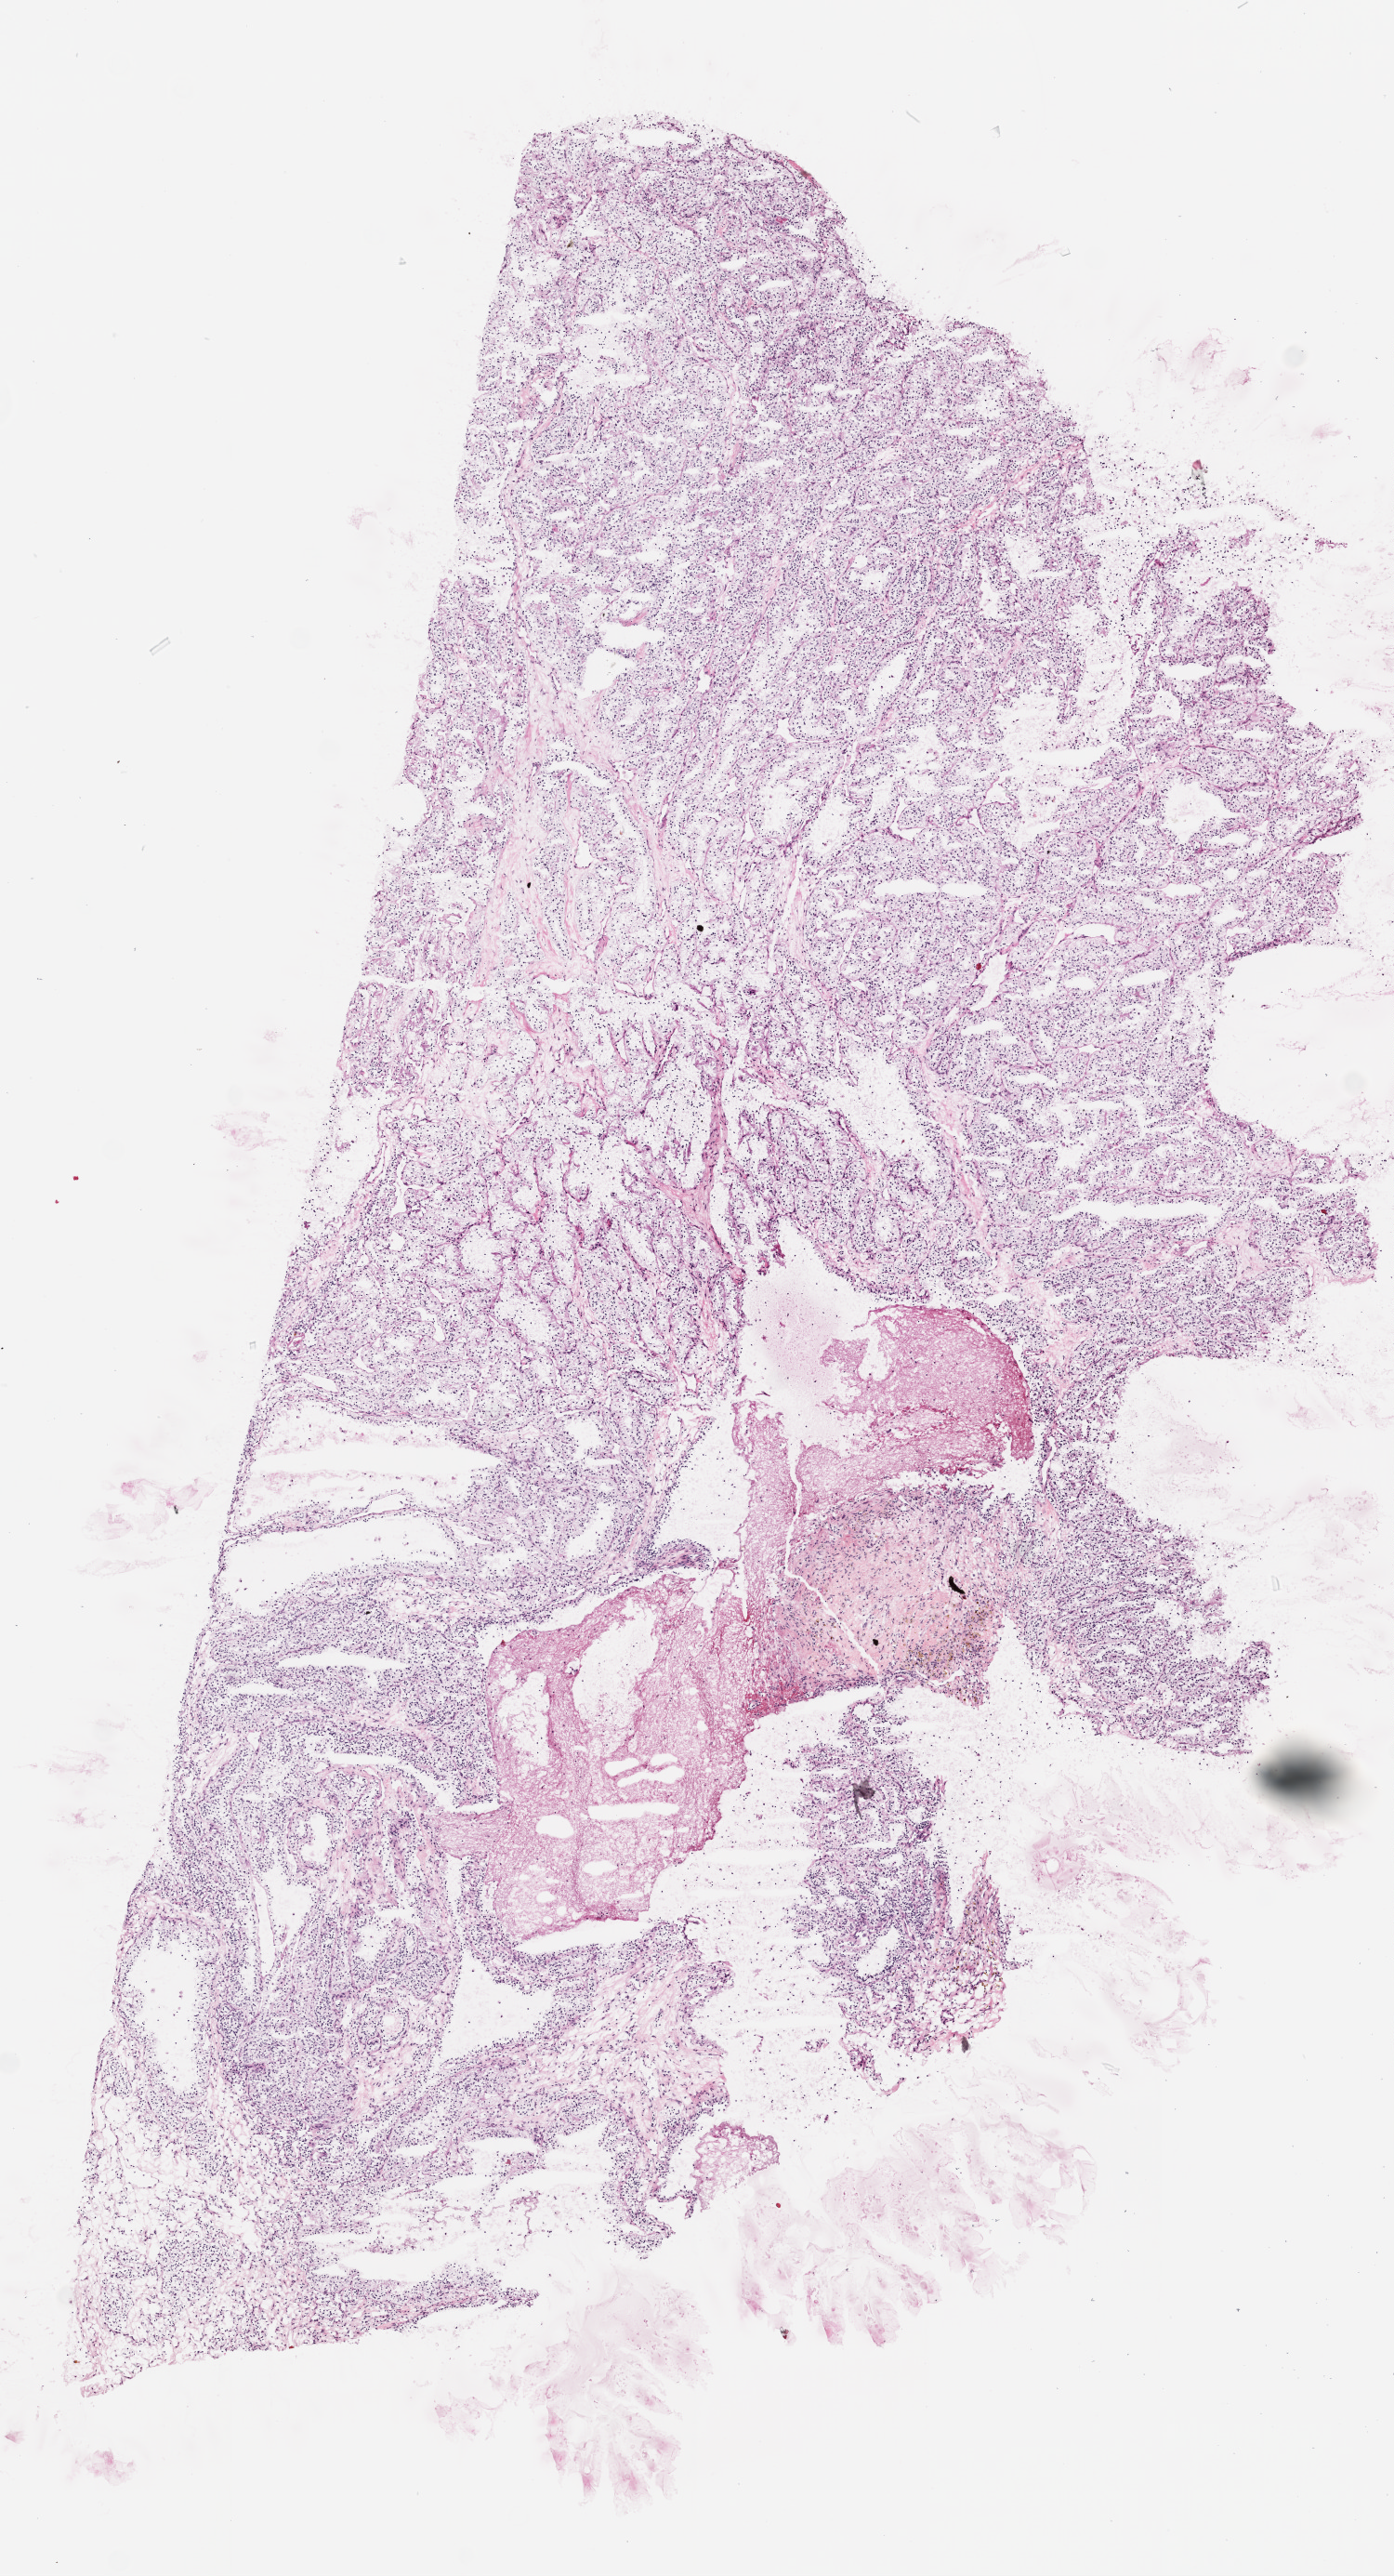
Digitized H&E-stained tissue section (whole slide), shown as a low-resolution overview of the whole scanned area (about 6.0 x 11.1 mm, acquisition: 20x scan); frozen section; kidney, primary tumour sample. Patient: male, age at initial diagnosis 45 years. Histologic grade: G2 (moderately differentiated). Composition of this section per pathologist review: tumour cells 85%, tumour nuclei 90%, normal cells 0%, stromal cells 0%, necrosis 15%. Inflammatory infiltration, as recorded: lymphocyte infiltration 0%, monocyte infiltration 0%, neutrophil infiltration 0%.
* laterality: right
* pathologic diagnosis: Clear cell adenocarcinoma, NOS
* AJCC pathologic stage: I (7th edition)